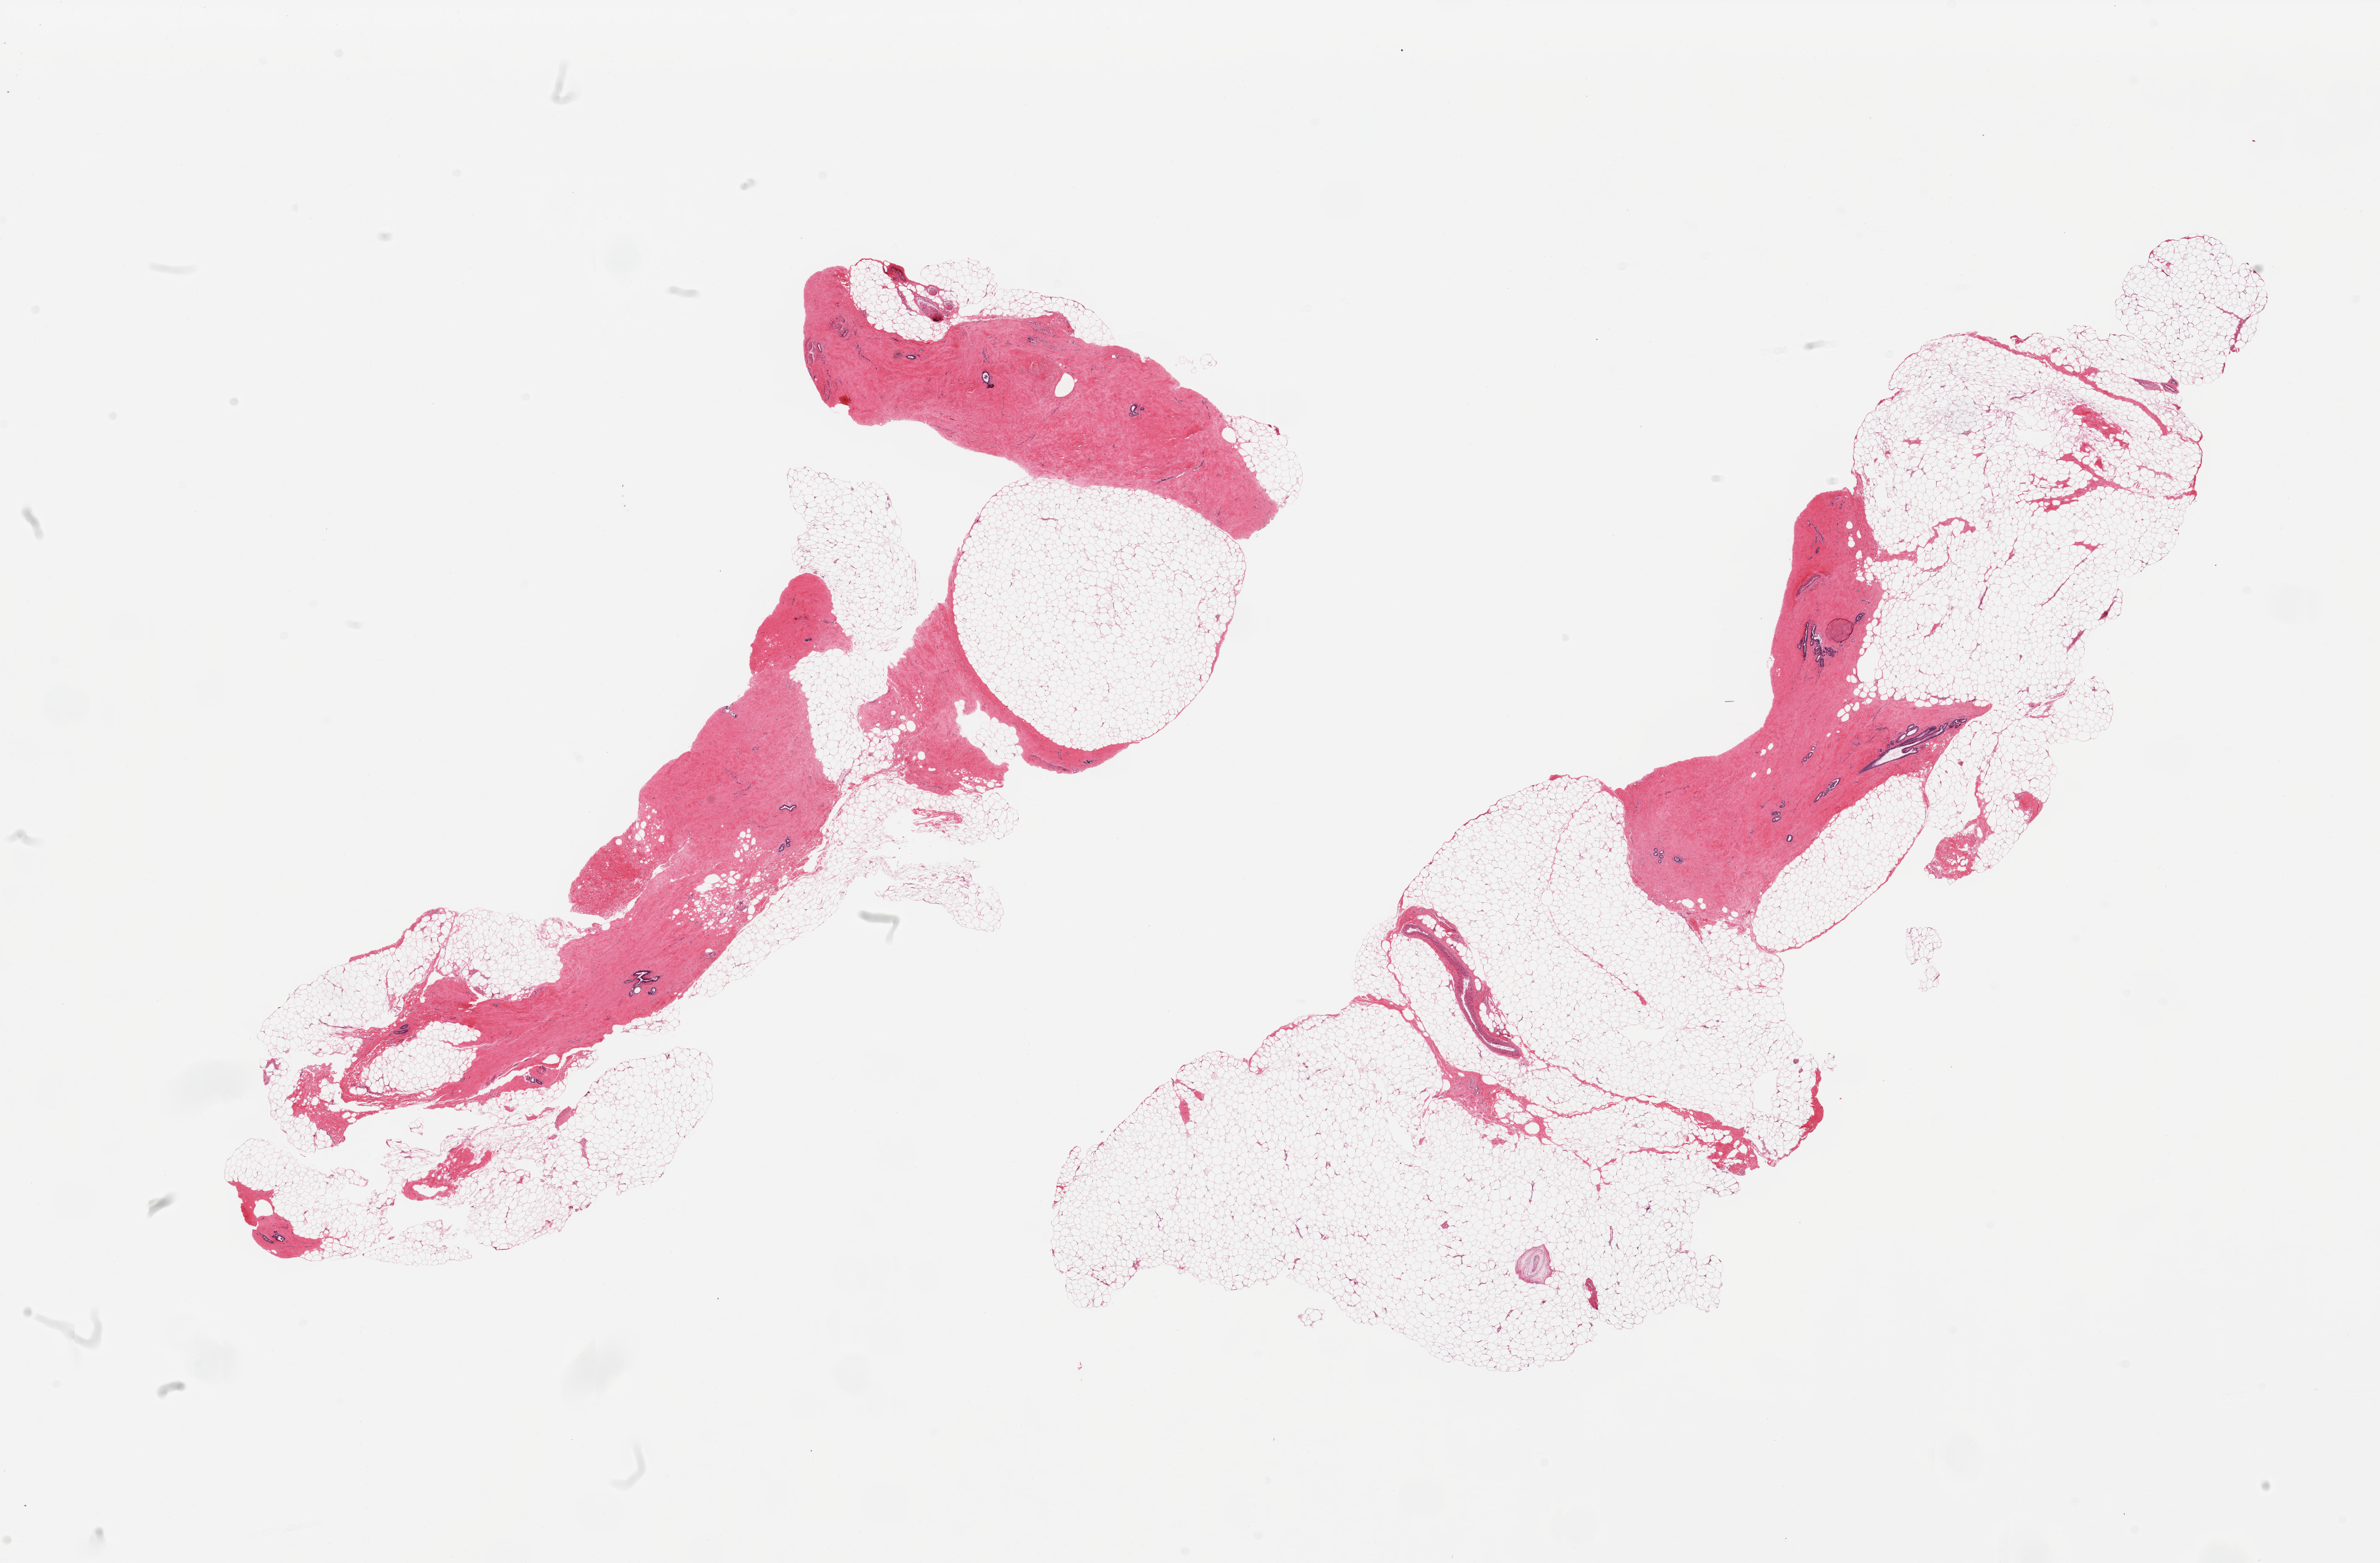
Hematoxylin and eosin (H&E) whole-slide image, brightfield, whole scanned area (about 31.5 x 20.7 mm) shown as a low-resolution overview, PAXgene-fixed paraffin-embedded (PFPE) section, target tissue: breast, tissue donor sample. Male donor.
Review note (as recorded): 2 pieces; fibroadipose tissue with ducts.